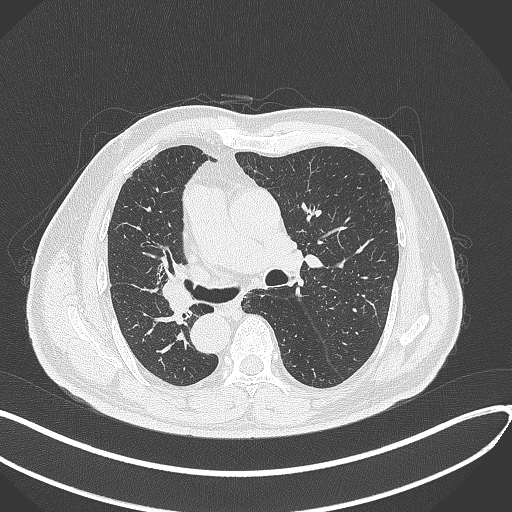
Chest CT, one axial slice. Position 167 of 300 along the scan axis. Reconstruction kernel B70f. Lung window (W 1500 / L -600 HU). 1 mm slice thickness. 512 × 512 image matrix. Patient: male, 67 years. From the clinical record (not read from this slice): clinical TNM (as recorded): T2a N0 M0.
Annotated regions visible in this slice (rectangle marked by the reading radiologist):
- lung tumour (recorded histology: squamous cell carcinoma): box from (x=156, y=274) to (x=199, y=325) px